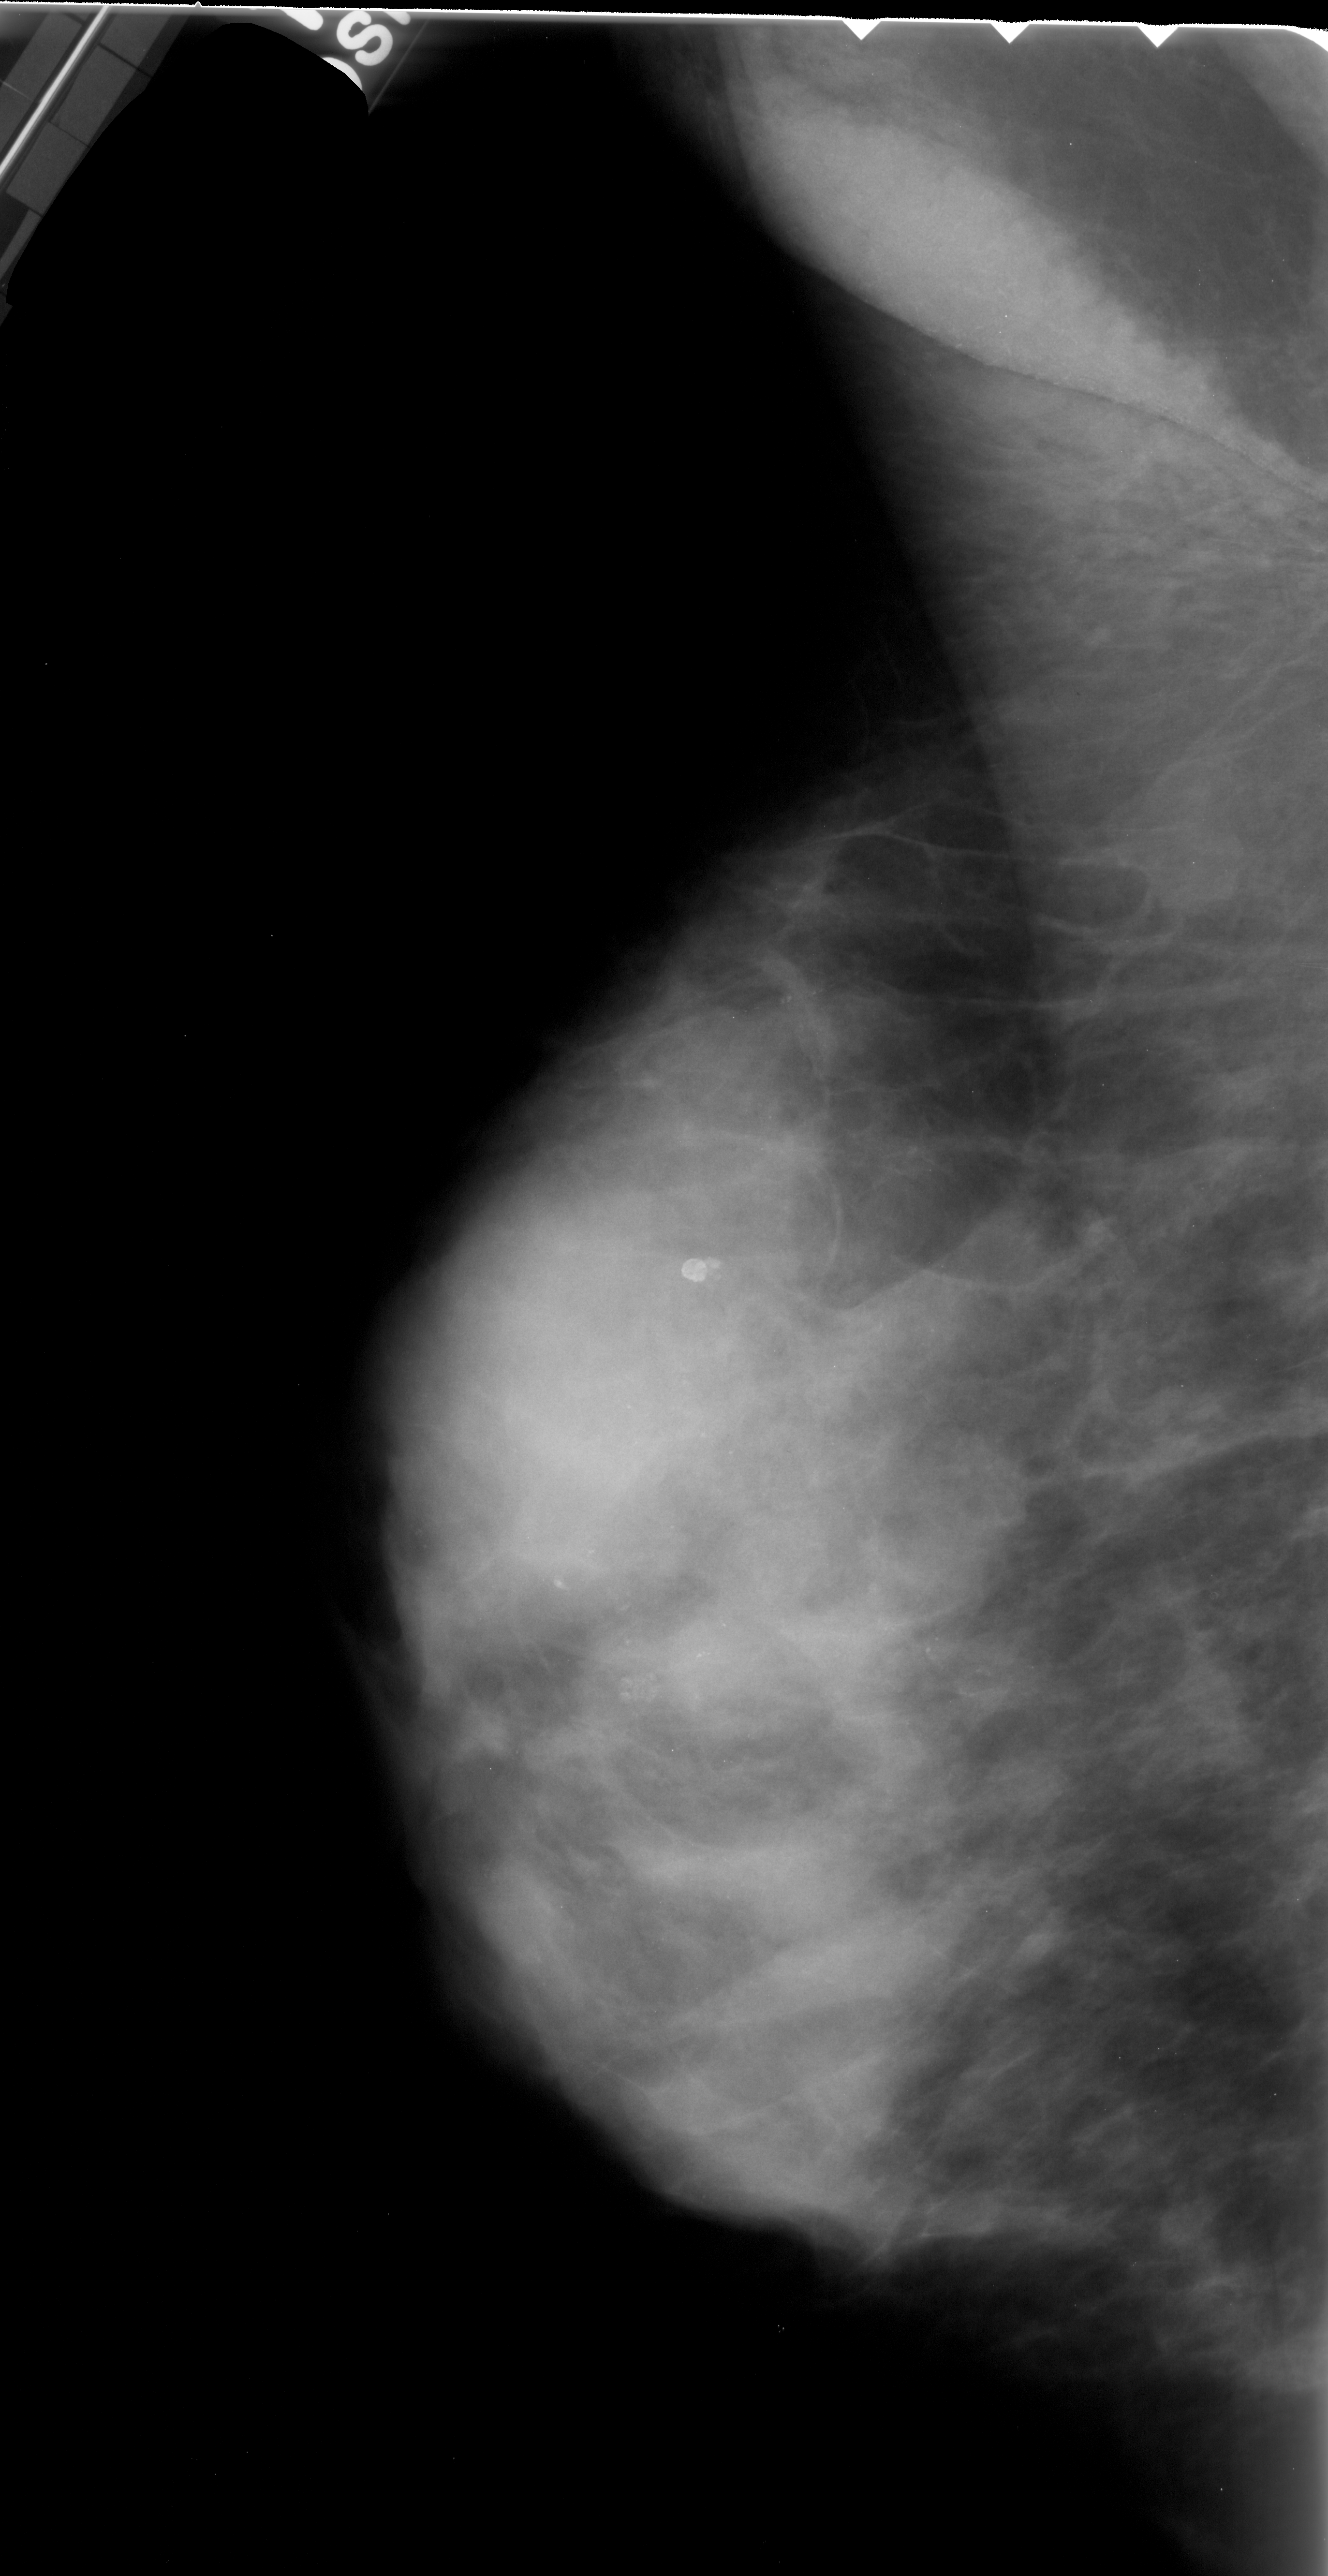
Mammogram (digitized film), left breast, MLO view, breast composition: extremely dense (BI-RADS density category 4 of 4).
Finding: calcifications, morphology amorphous, distribution clustered; BI-RADS assessment category 4; pathology result (as recorded, not read from the image): malignant.